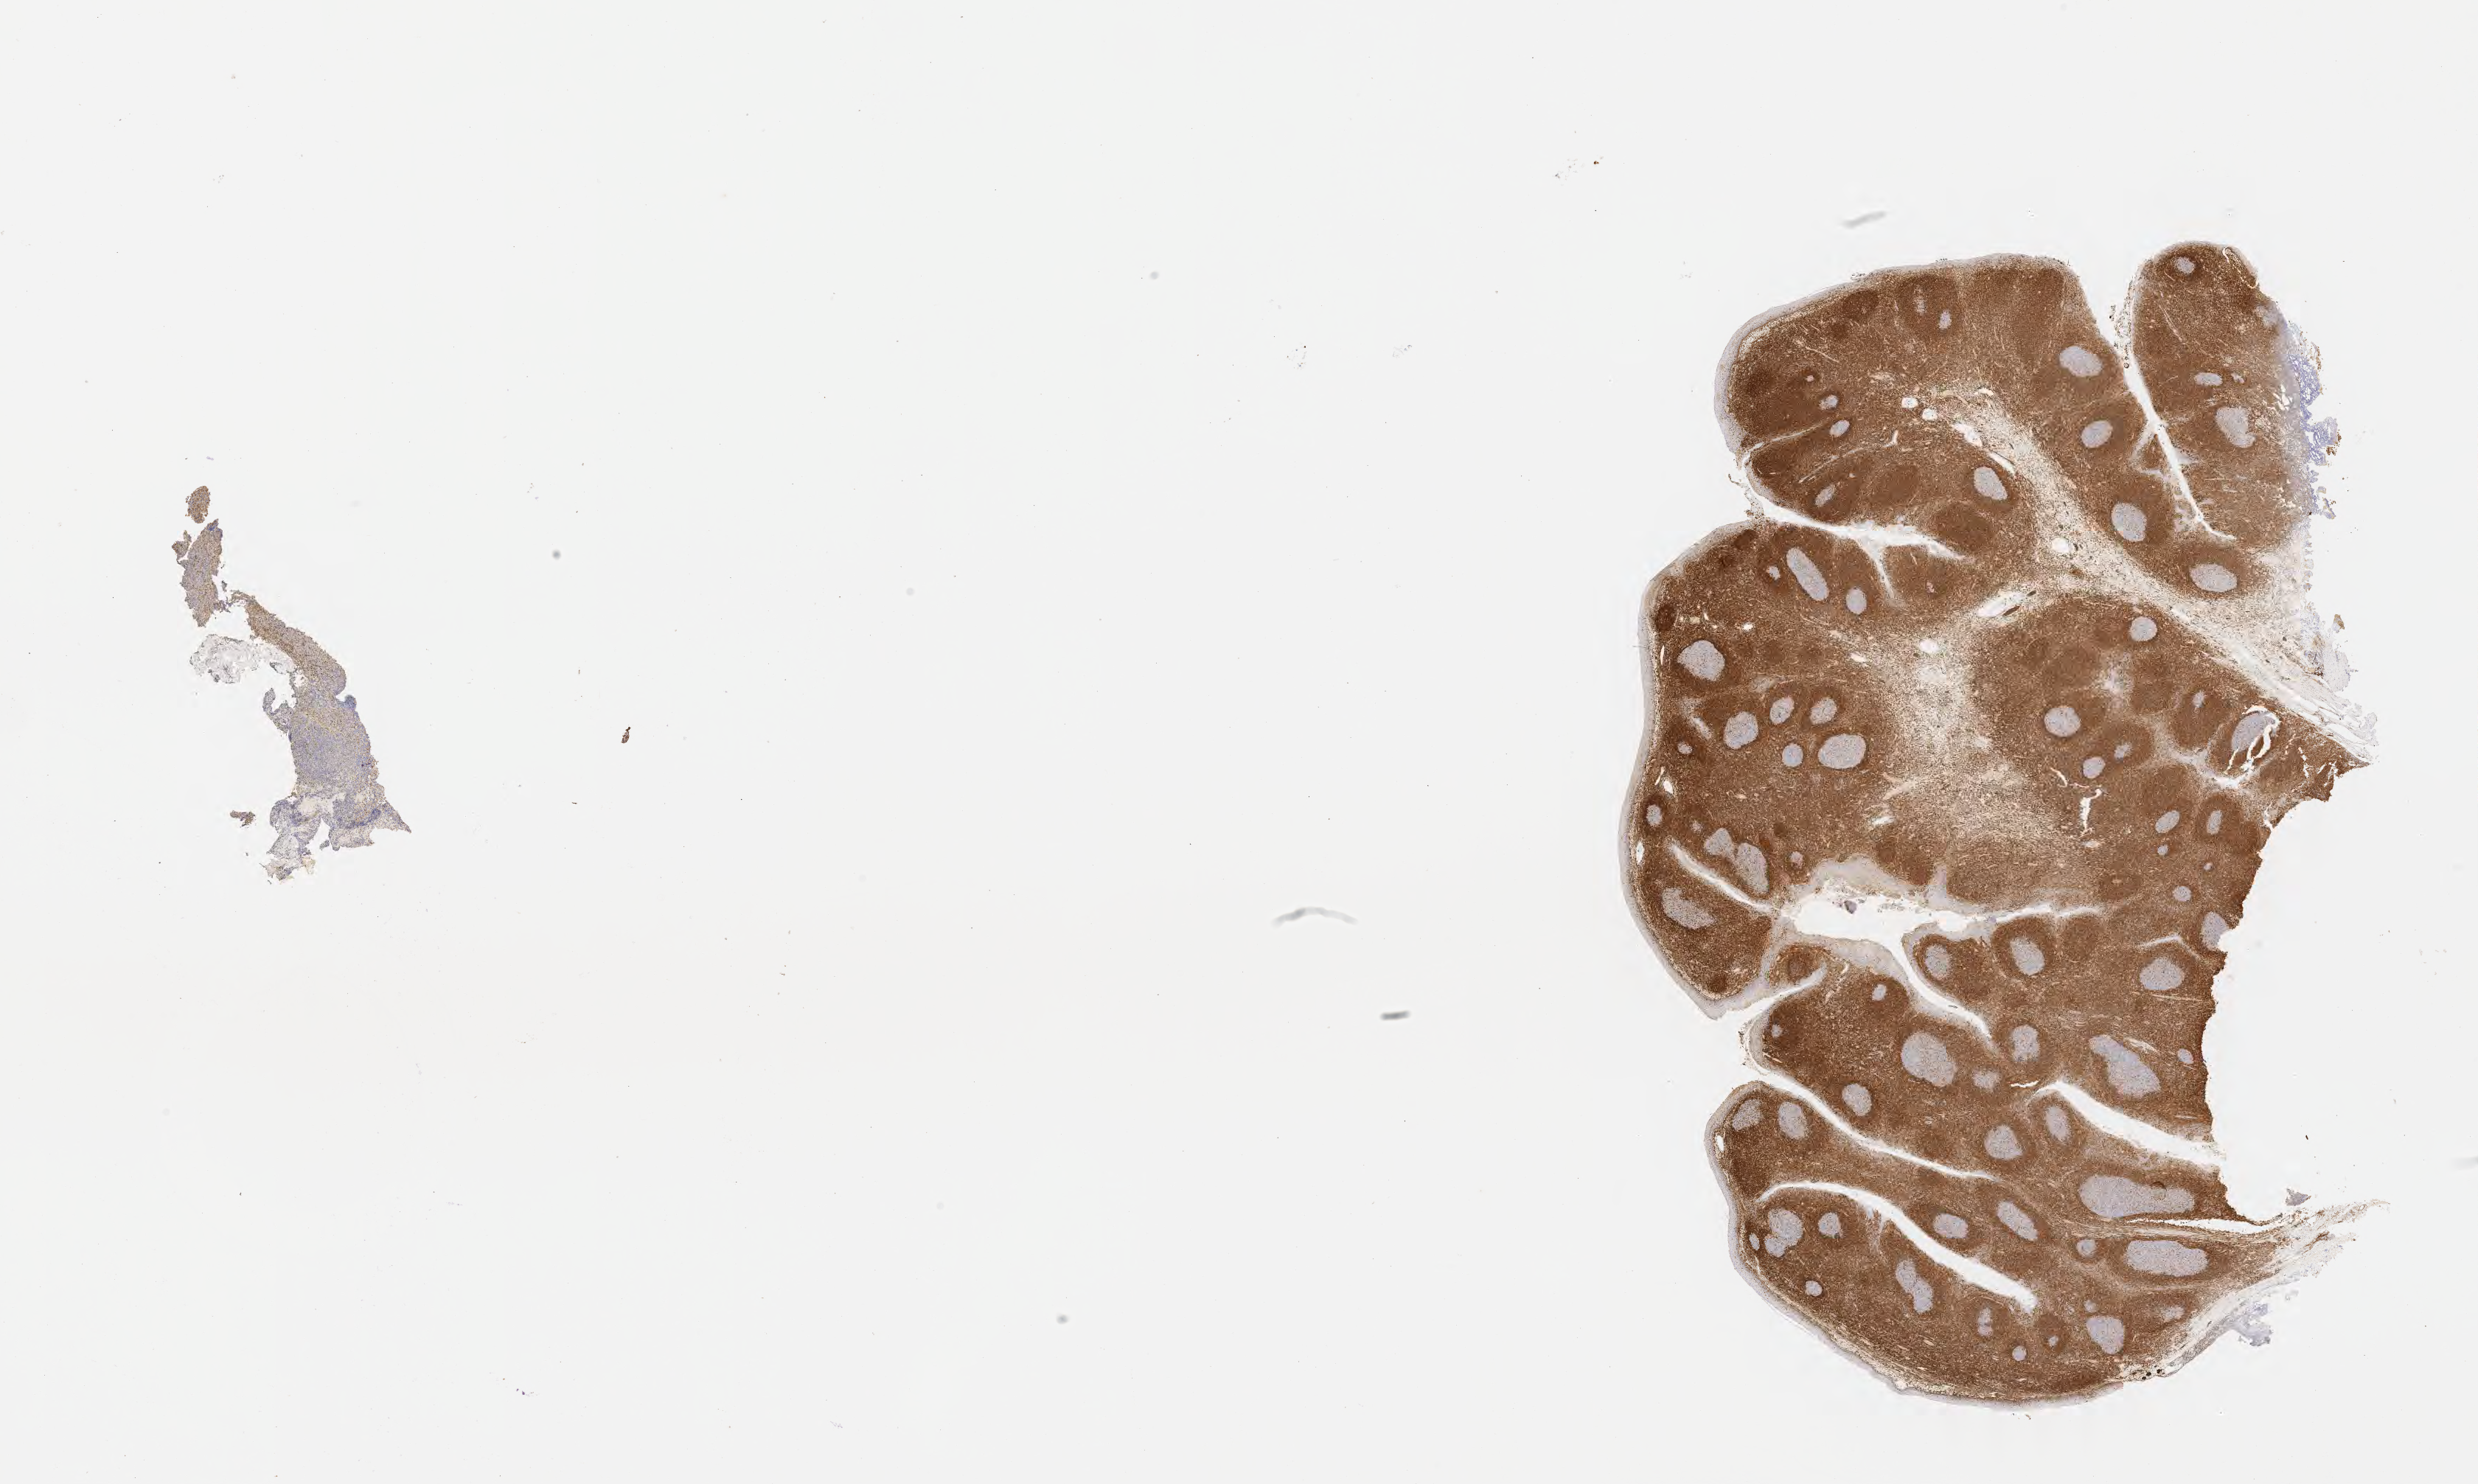
IHC for BCL2, whole-slide image — whole scanned area (about 27.2 x 16.3 mm) shown as a low-resolution overview, specimen: tumor tissue. Patient: female, aged 27.
Diagnosis: Diffuse large B-cell lymphoma, NOS.